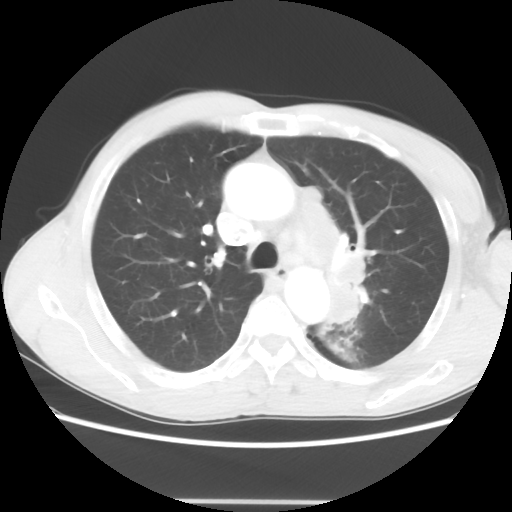
Chest CT, one axial slice; position 44 of 62 along the scan axis; reconstruction kernel STANDARD; lung window (W 1500 / L -600 HU); 512 × 512 image matrix. Patient: male, 61 years. From the clinical record (not read from this slice): clinical TNM (as recorded): T3 N1 M1.
Outlined on this slice (rectangle marked by the reading radiologist):
- lung tumour (recorded histology: adenocarcinoma): bounding box [x1, y1, x2, y2] px = [304, 180, 369, 329]